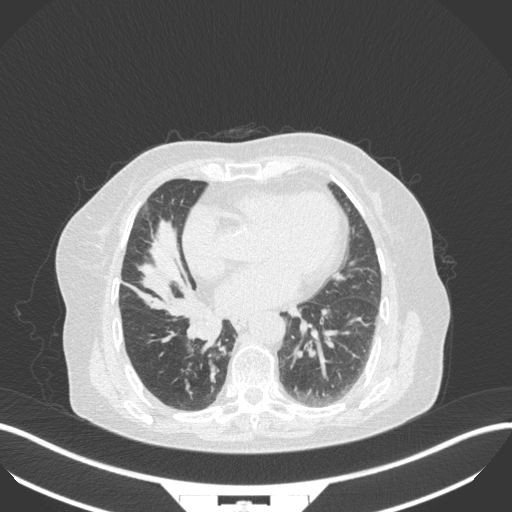
Chest CT, one axial slice. Position 127 of 329 along the scan axis. Reconstruction kernel B31f. 120 kVp. Lung window (W 1500 / L -600 HU). 1 mm slice thickness. 512 × 512 image matrix. Patient: female, 75 years. From the clinical record (not read from this slice): clinical TNM (as recorded): T1b N0 M1a.
Outlined on this slice (bounding box drawn by a radiologist):
- lung tumour (recorded histology: squamous cell carcinoma): bounding box [x1, y1, x2, y2] px = [180, 305, 227, 347]